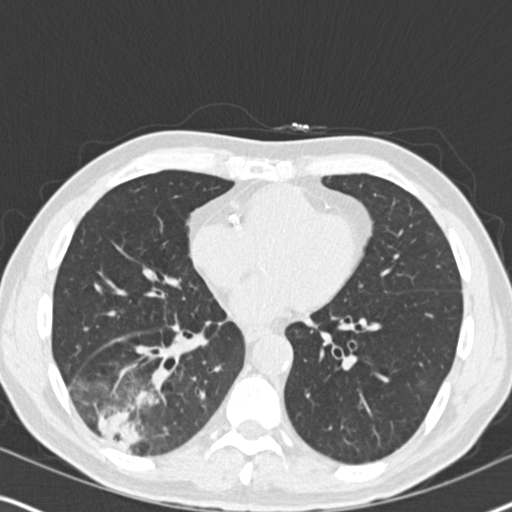
Low-dose screening chest CT, one axial slice; slice 82 of 182 in the series (ordered by position); lung window (W 1500 / L -600 HU); 2 mm slice thickness; 512 × 512 image matrix, field of view 330 × 330 mm.
Structures marked on this image (manually delineated by an expert):
- lesion 1 (tumor, lower lobe of right lung): bounding box [x1, y1, x2, y2] px = [99, 391, 159, 451]